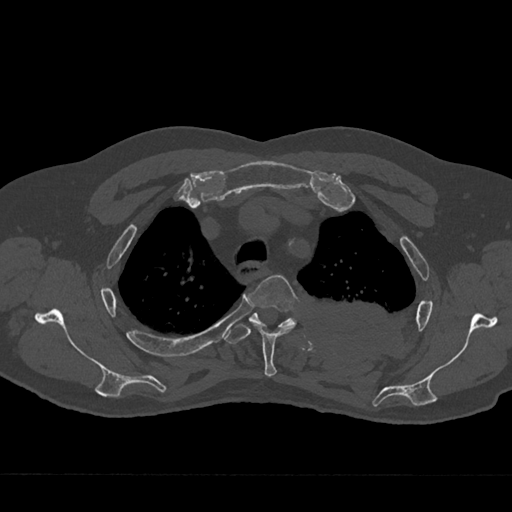
CT including the spine, one axial slice. Position 548 of 797 along the scan axis. 120 kVp. Bone window (W 1800 / L 400 HU). 512 × 512 image matrix, field of view 377 × 377 mm. Male patient, age 75 years. Case-level facts recorded for this patient, not image findings: primary cancer: renal; vertebrae with lytic lesions (as recorded): T4.
Annotated regions visible in this slice (semi-automatic segmentation, software-assisted and operator-edited):
- T3 vertebra: bounding box [x1, y1, x2, y2] px = [249, 275, 300, 377]
- T4 vertebra: [225, 313, 296, 344]